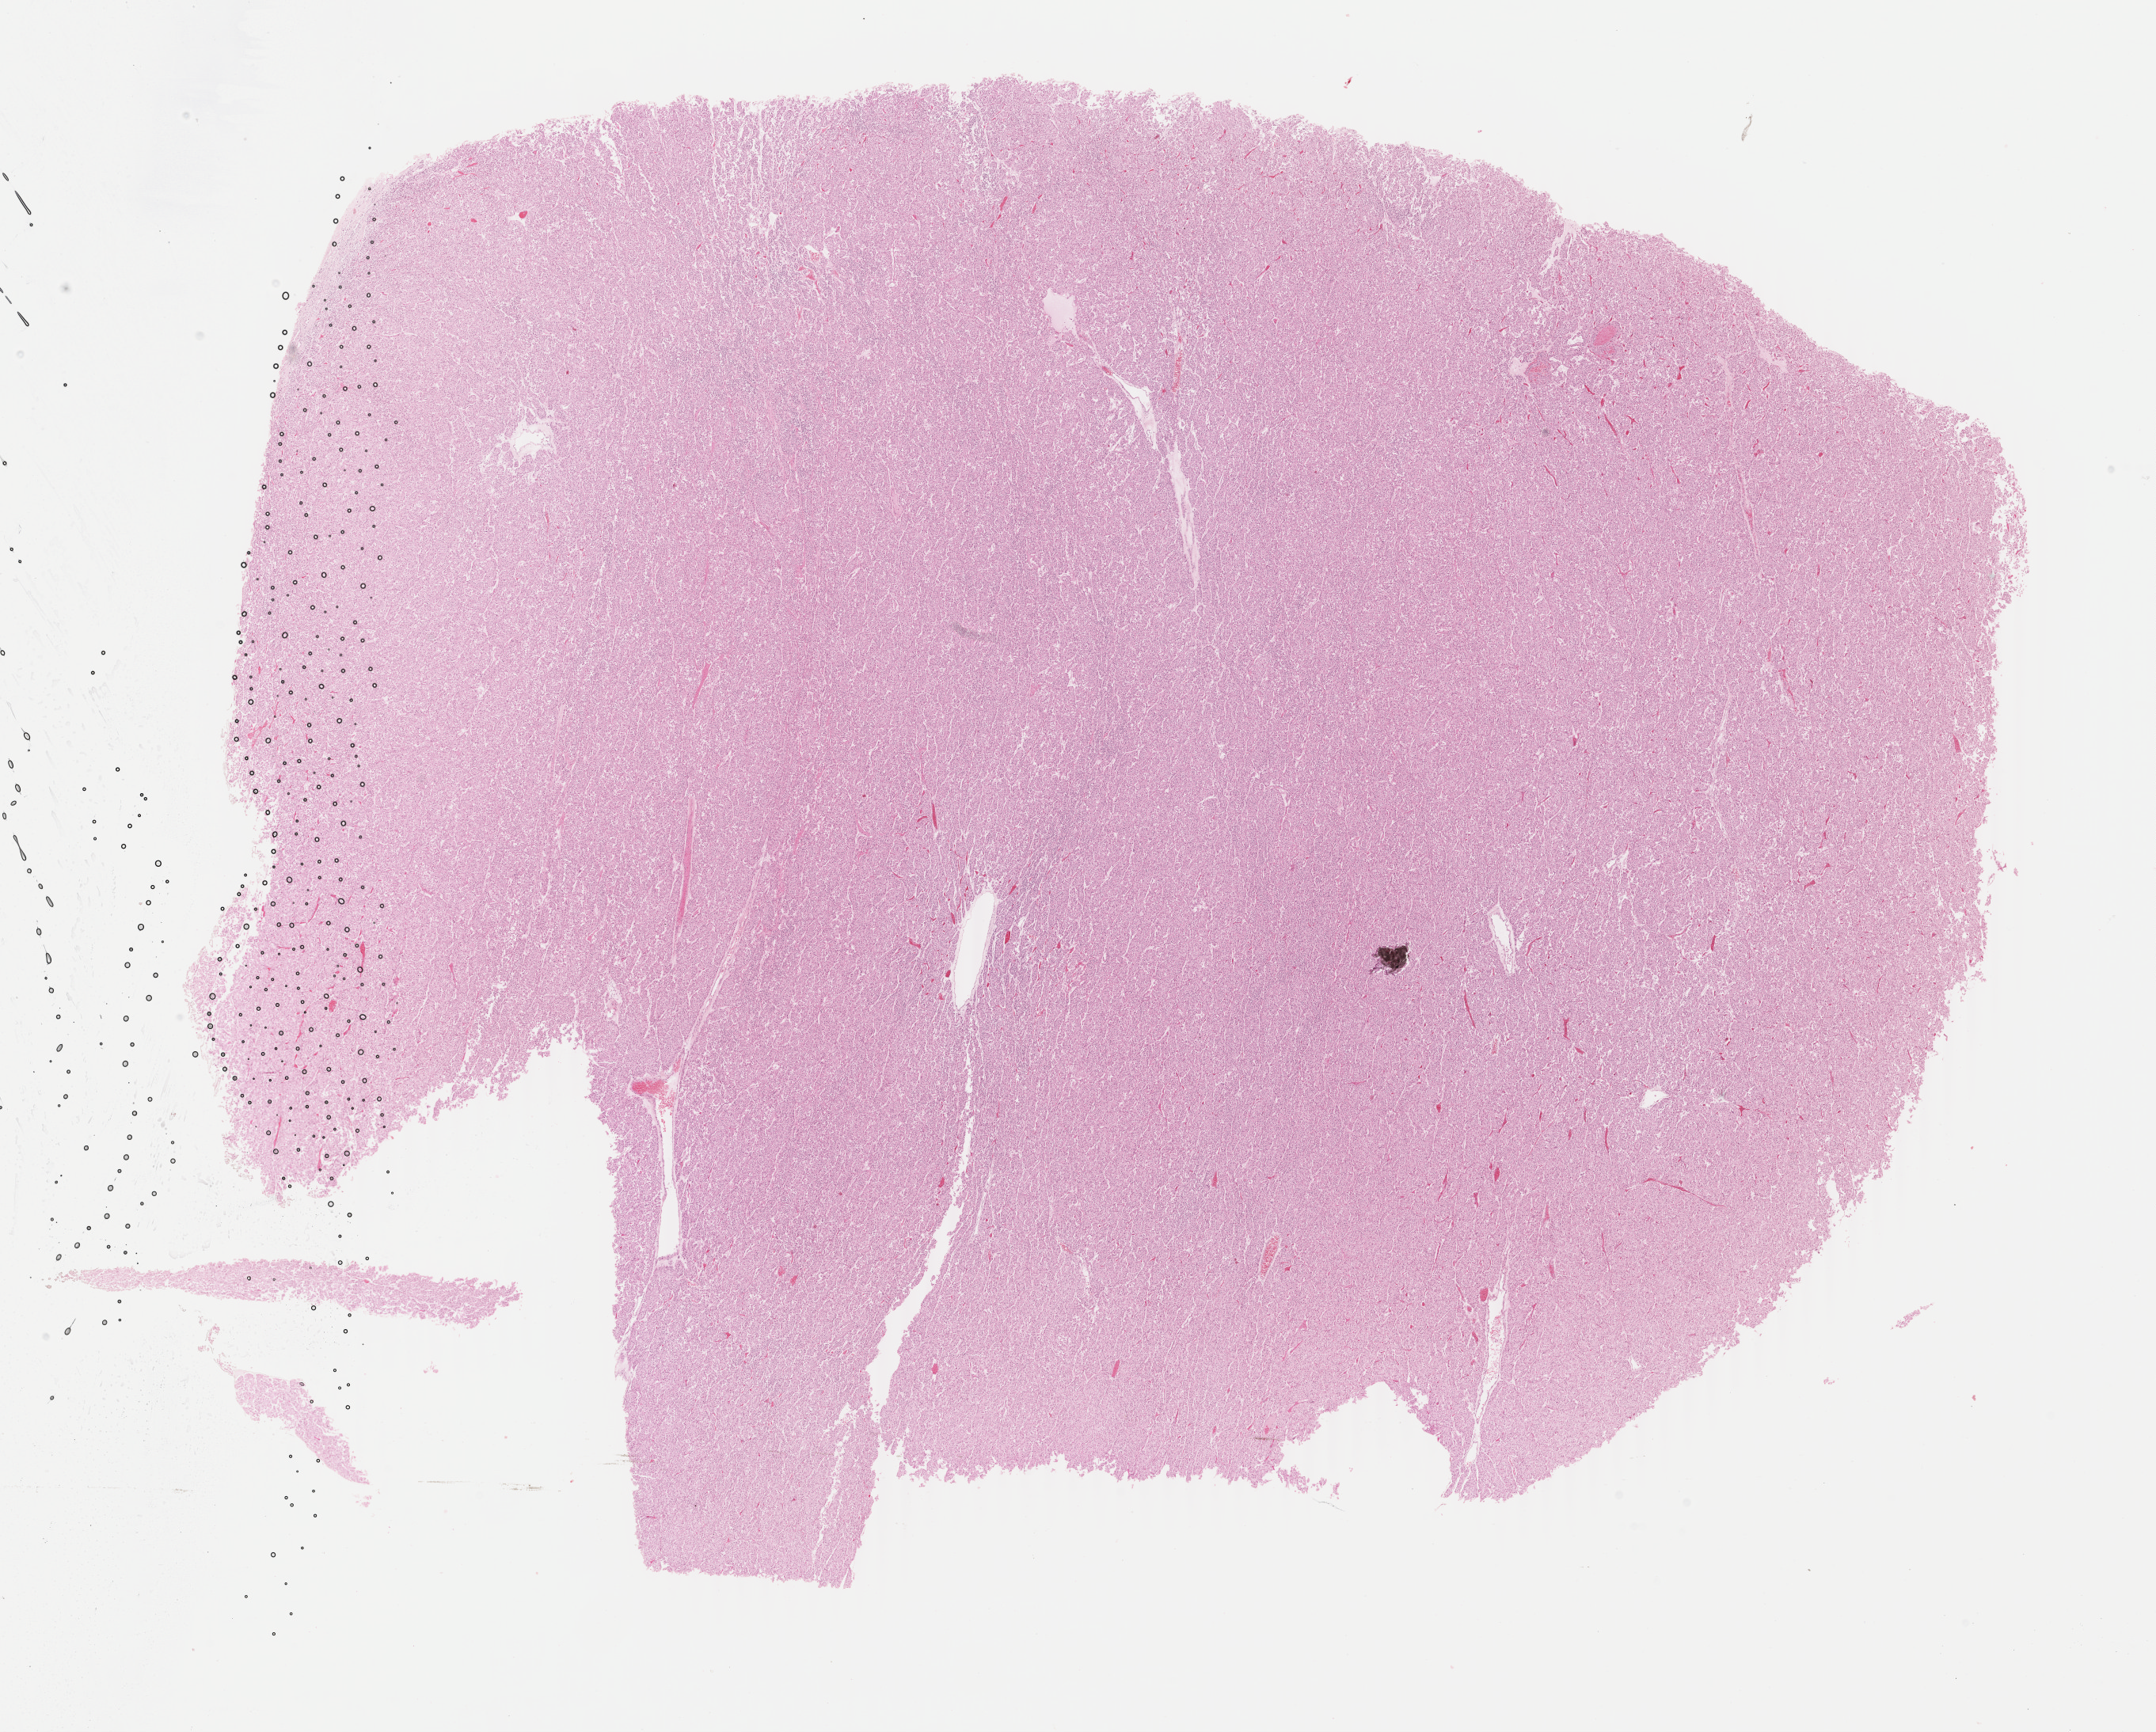
Digitized H&E-stained tissue section (whole slide) — whole scanned area (about 21.7 x 17.4 mm) shown as a low-resolution overview; FFPE section; primary tumour sample from the kidney. Patient: female, age at initial diagnosis 45 years.
Pathologic diagnosis: Renal cell carcinoma, chromophobe type. AJCC pathologic stage: II (5th edition). Lymph nodes positive (case pathology): 0 of 5 examined. Laterality: left.